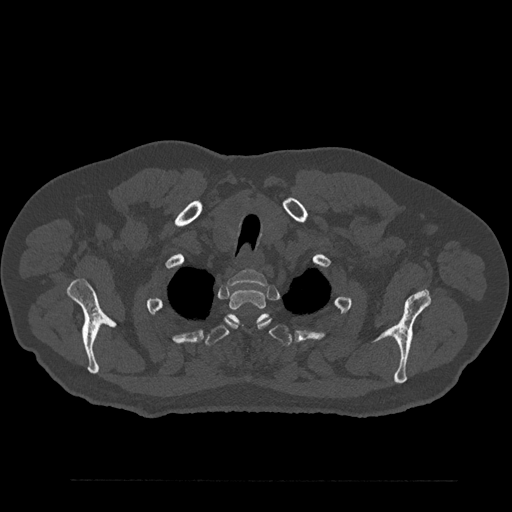
CT including the spine, one axial slice. Position 709 of 797 along the scan axis. Bone window (W 1800 / L 400 HU). 0.5 mm slice thickness. 512 × 512 image matrix, field of view 430 × 430 mm. Patient: male, 61 years. Case-level facts recorded for this patient, not image findings: primary cancer: prostate.
Outlined on this slice (semi-automatic segmentation, software-assisted and operator-edited):
- T1 vertebra: box from (x=228, y=269) to (x=268, y=286) px
- T2 vertebra: (x=225, y=288)–(x=271, y=328)
- T3 vertebra: (x=205, y=313)–(x=291, y=377)